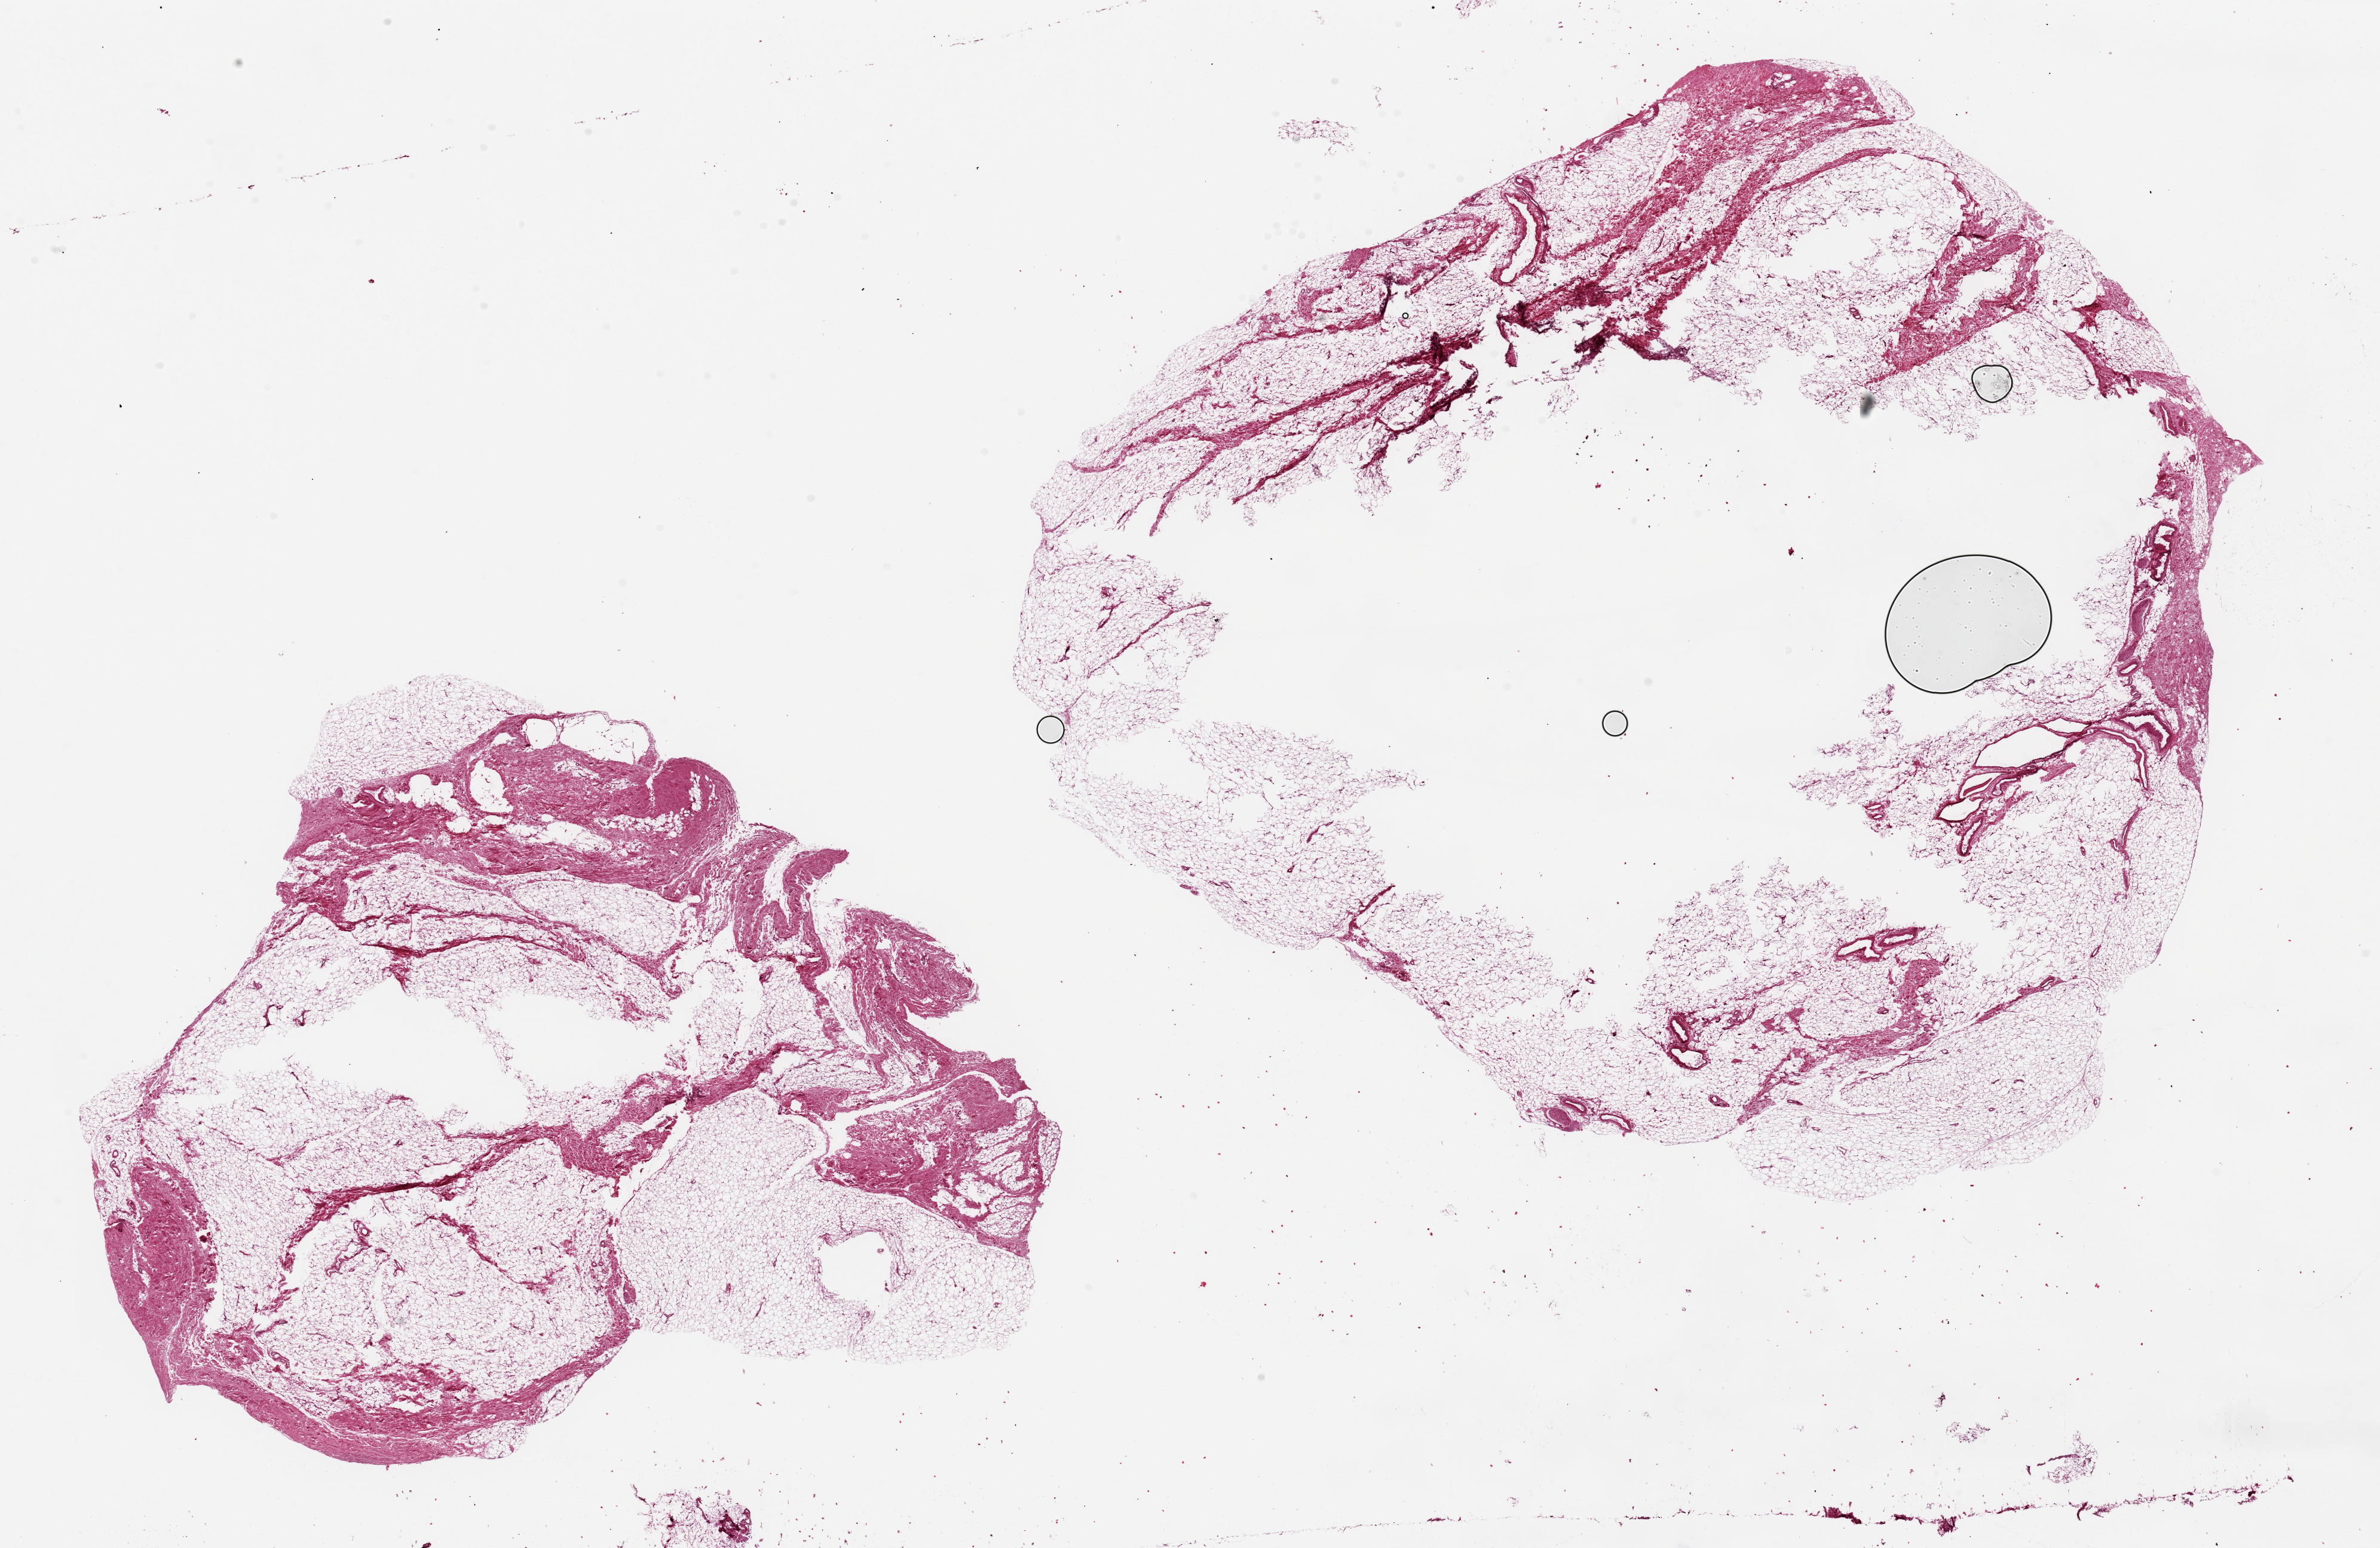
Whole-slide image, H&E stain, a low-resolution overview of the entire scanned area, about 31.5 x 20.5 mm (acquisition: 20x scan); PAXgene-fixed, paraffin-embedded tissue; target tissue: breast; tissue donor sample. Donor sex: male.
Reviewer comment on this tissue sample: 2 pieces, 10.4x11.5 & 14.5x15 mm; no mammary tissue, only fibroadipose tissue; large central defect in larger over-sized piece.